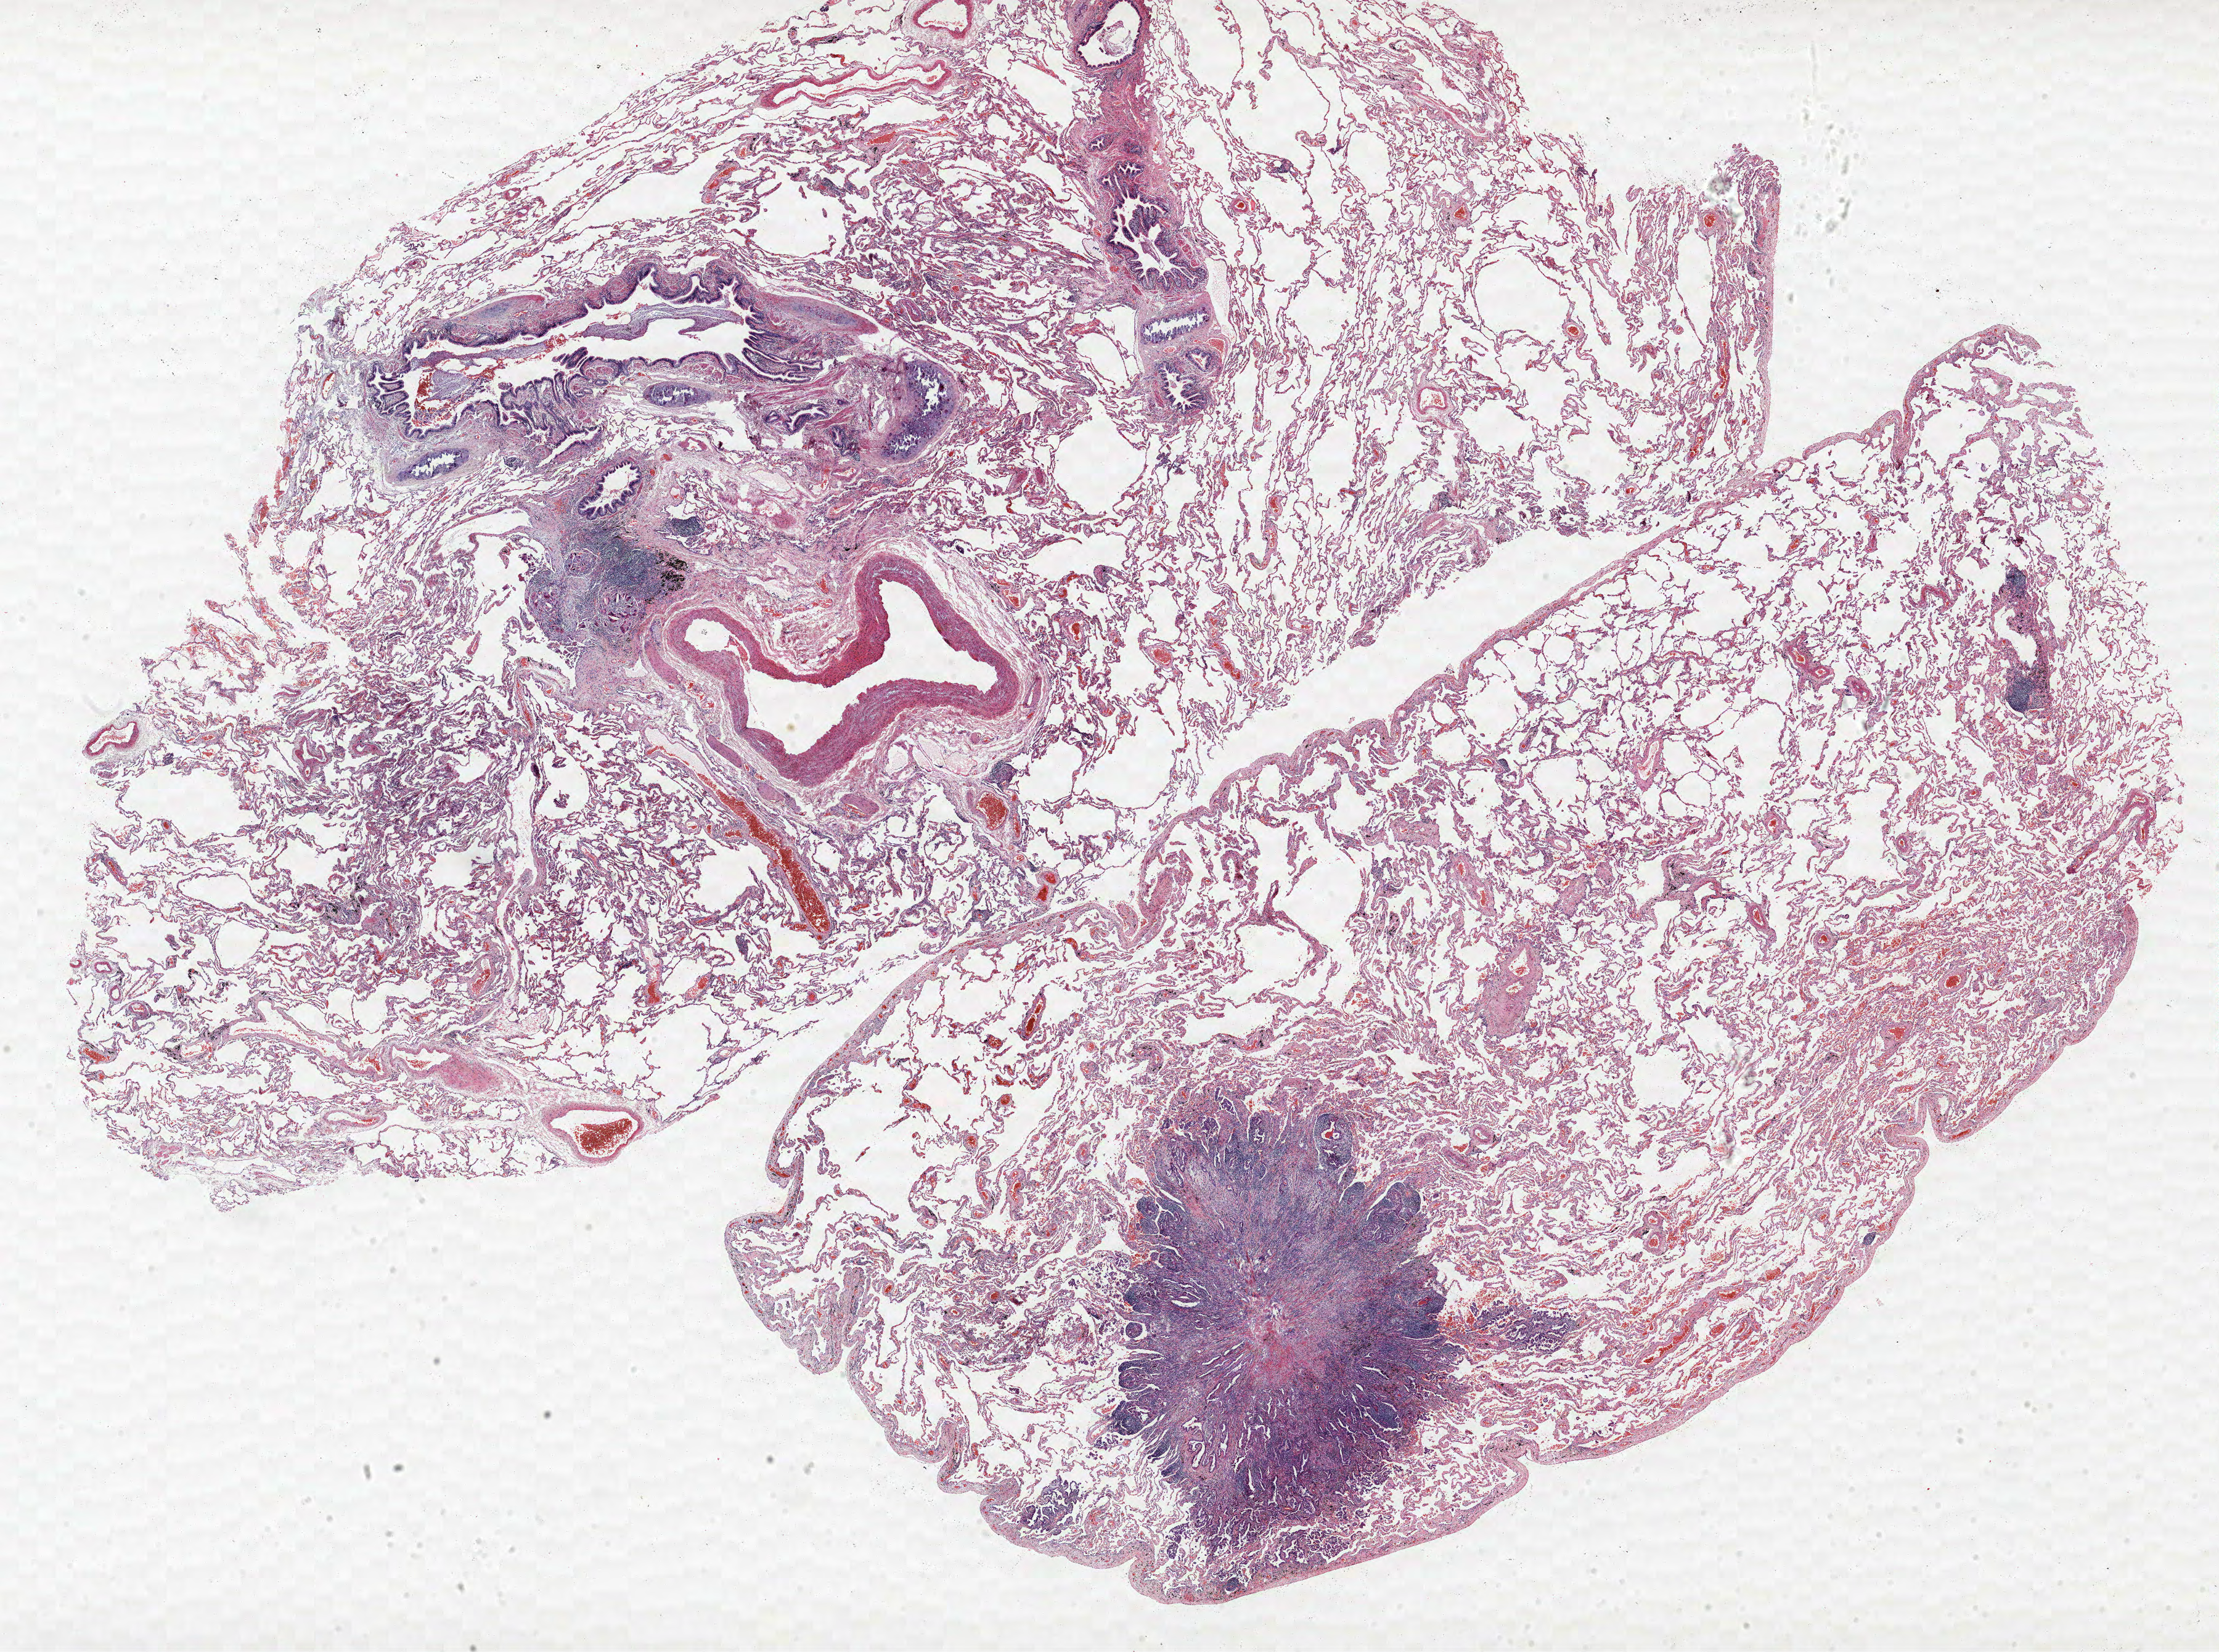
Whole-slide histology image, H&E, low-resolution overview of the scanned area, about 28.8 x 21.4 mm (from a 40x scan). Formalin-fixed paraffin-embedded (FFPE) section. Lung. Male patient, aged 73 at enrolment. Former smoker at enrolment. Grade: poorly differentiated (G3).
- primary tumour location (clinical record): right upper lobe
- participant's lung-cancer diagnosis: Adenocarcinoma, NOS
- stage (AJCC 6th edition): IB
- tumour size (pathology): 22 mm
- note: participant had 2 primary lung cancers recorded; fields above describe the first